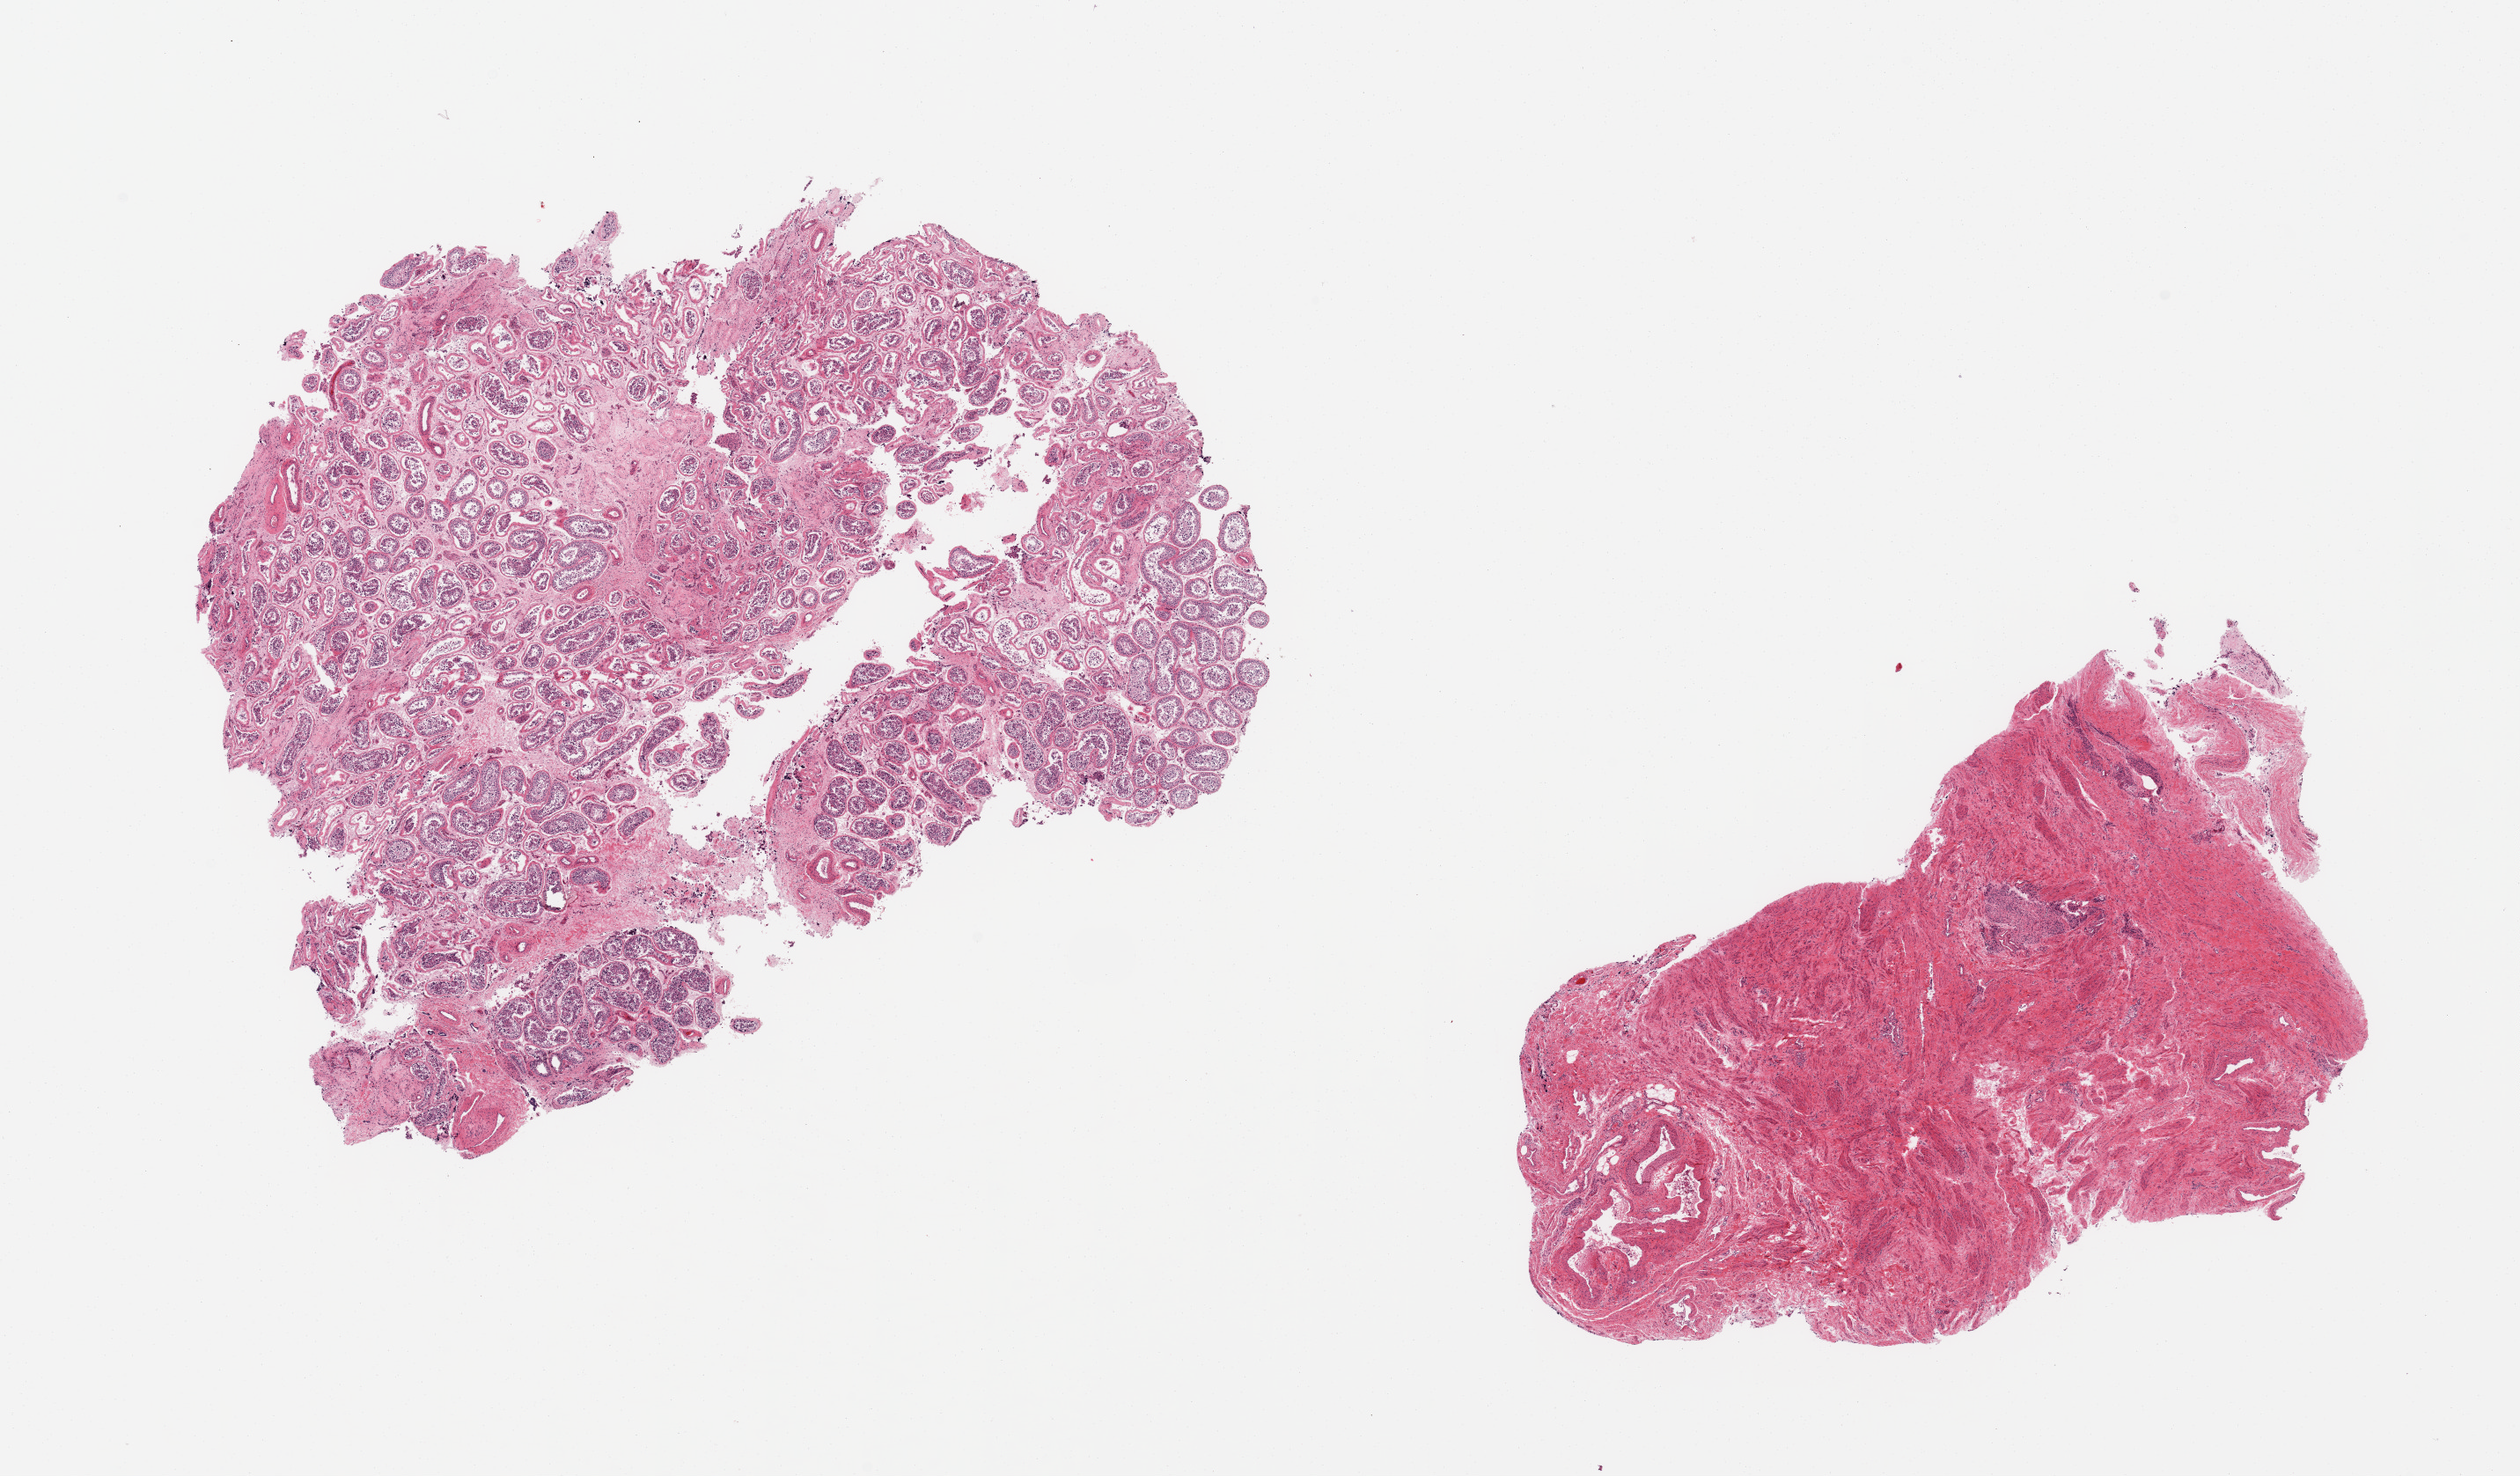
Whole-slide image, hematoxylin and eosin (H&E) stain, a low-resolution overview of the entire scanned area, about 22.6 x 13.3 mm; PAXgene-fixed paraffin-embedded (PFPE) section; sampled site (target tissue): testis; tissue donor sample. Donor: male.
Reviewer comment on this tissue sample: 2 pieces; sloughing of germ cells into tubule lumina, spermatogenesis decreased; second piece devoid of testicular tubules, consists only of fibromuscular stroma, vessels and nerves.